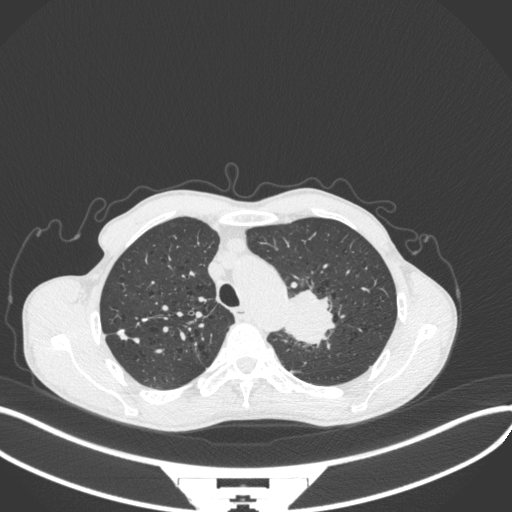
Chest CT, one axial slice. Position 325 of 394 along the scan axis. 120 kVp. Lung window (W 1500 / L -600 HU). 1 mm slice thickness. 512 × 512 image matrix, field of view 400 × 400 mm. Male patient, age 65 years. From the clinical record (not read from this slice): clinical TNM (as recorded): T2b N0 M0.
Structures marked on this image (bounding box drawn by a radiologist):
- lung tumour (recorded histology: adenocarcinoma): bounding box [x1, y1, x2, y2] px = [286, 286, 337, 346]